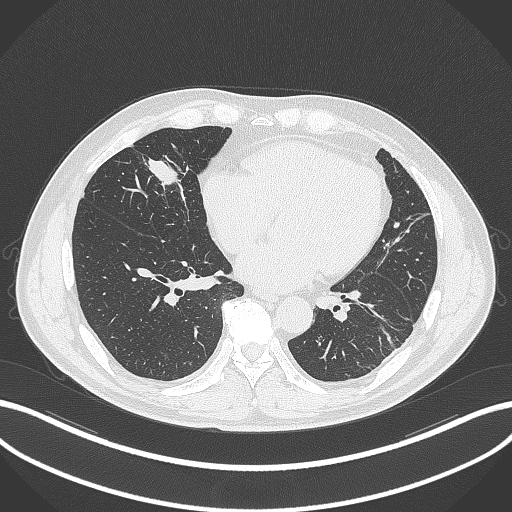
Chest CT, one axial slice; slice 104 of 399 in the series (ordered by position); reconstruction kernel B70f; 120 kVp; lung window (W 1500 / L -600 HU); 1 mm slice thickness; 512 × 512 image matrix. Male patient, age 59 years. From the clinical record (not read from this slice): clinical TNM (as recorded): T2a N1 M0.
Annotated regions visible in this slice (bounding box drawn by a radiologist):
- lung tumour (recorded histology: adenocarcinoma): bounding box [x1, y1, x2, y2] px = [142, 153, 187, 196]